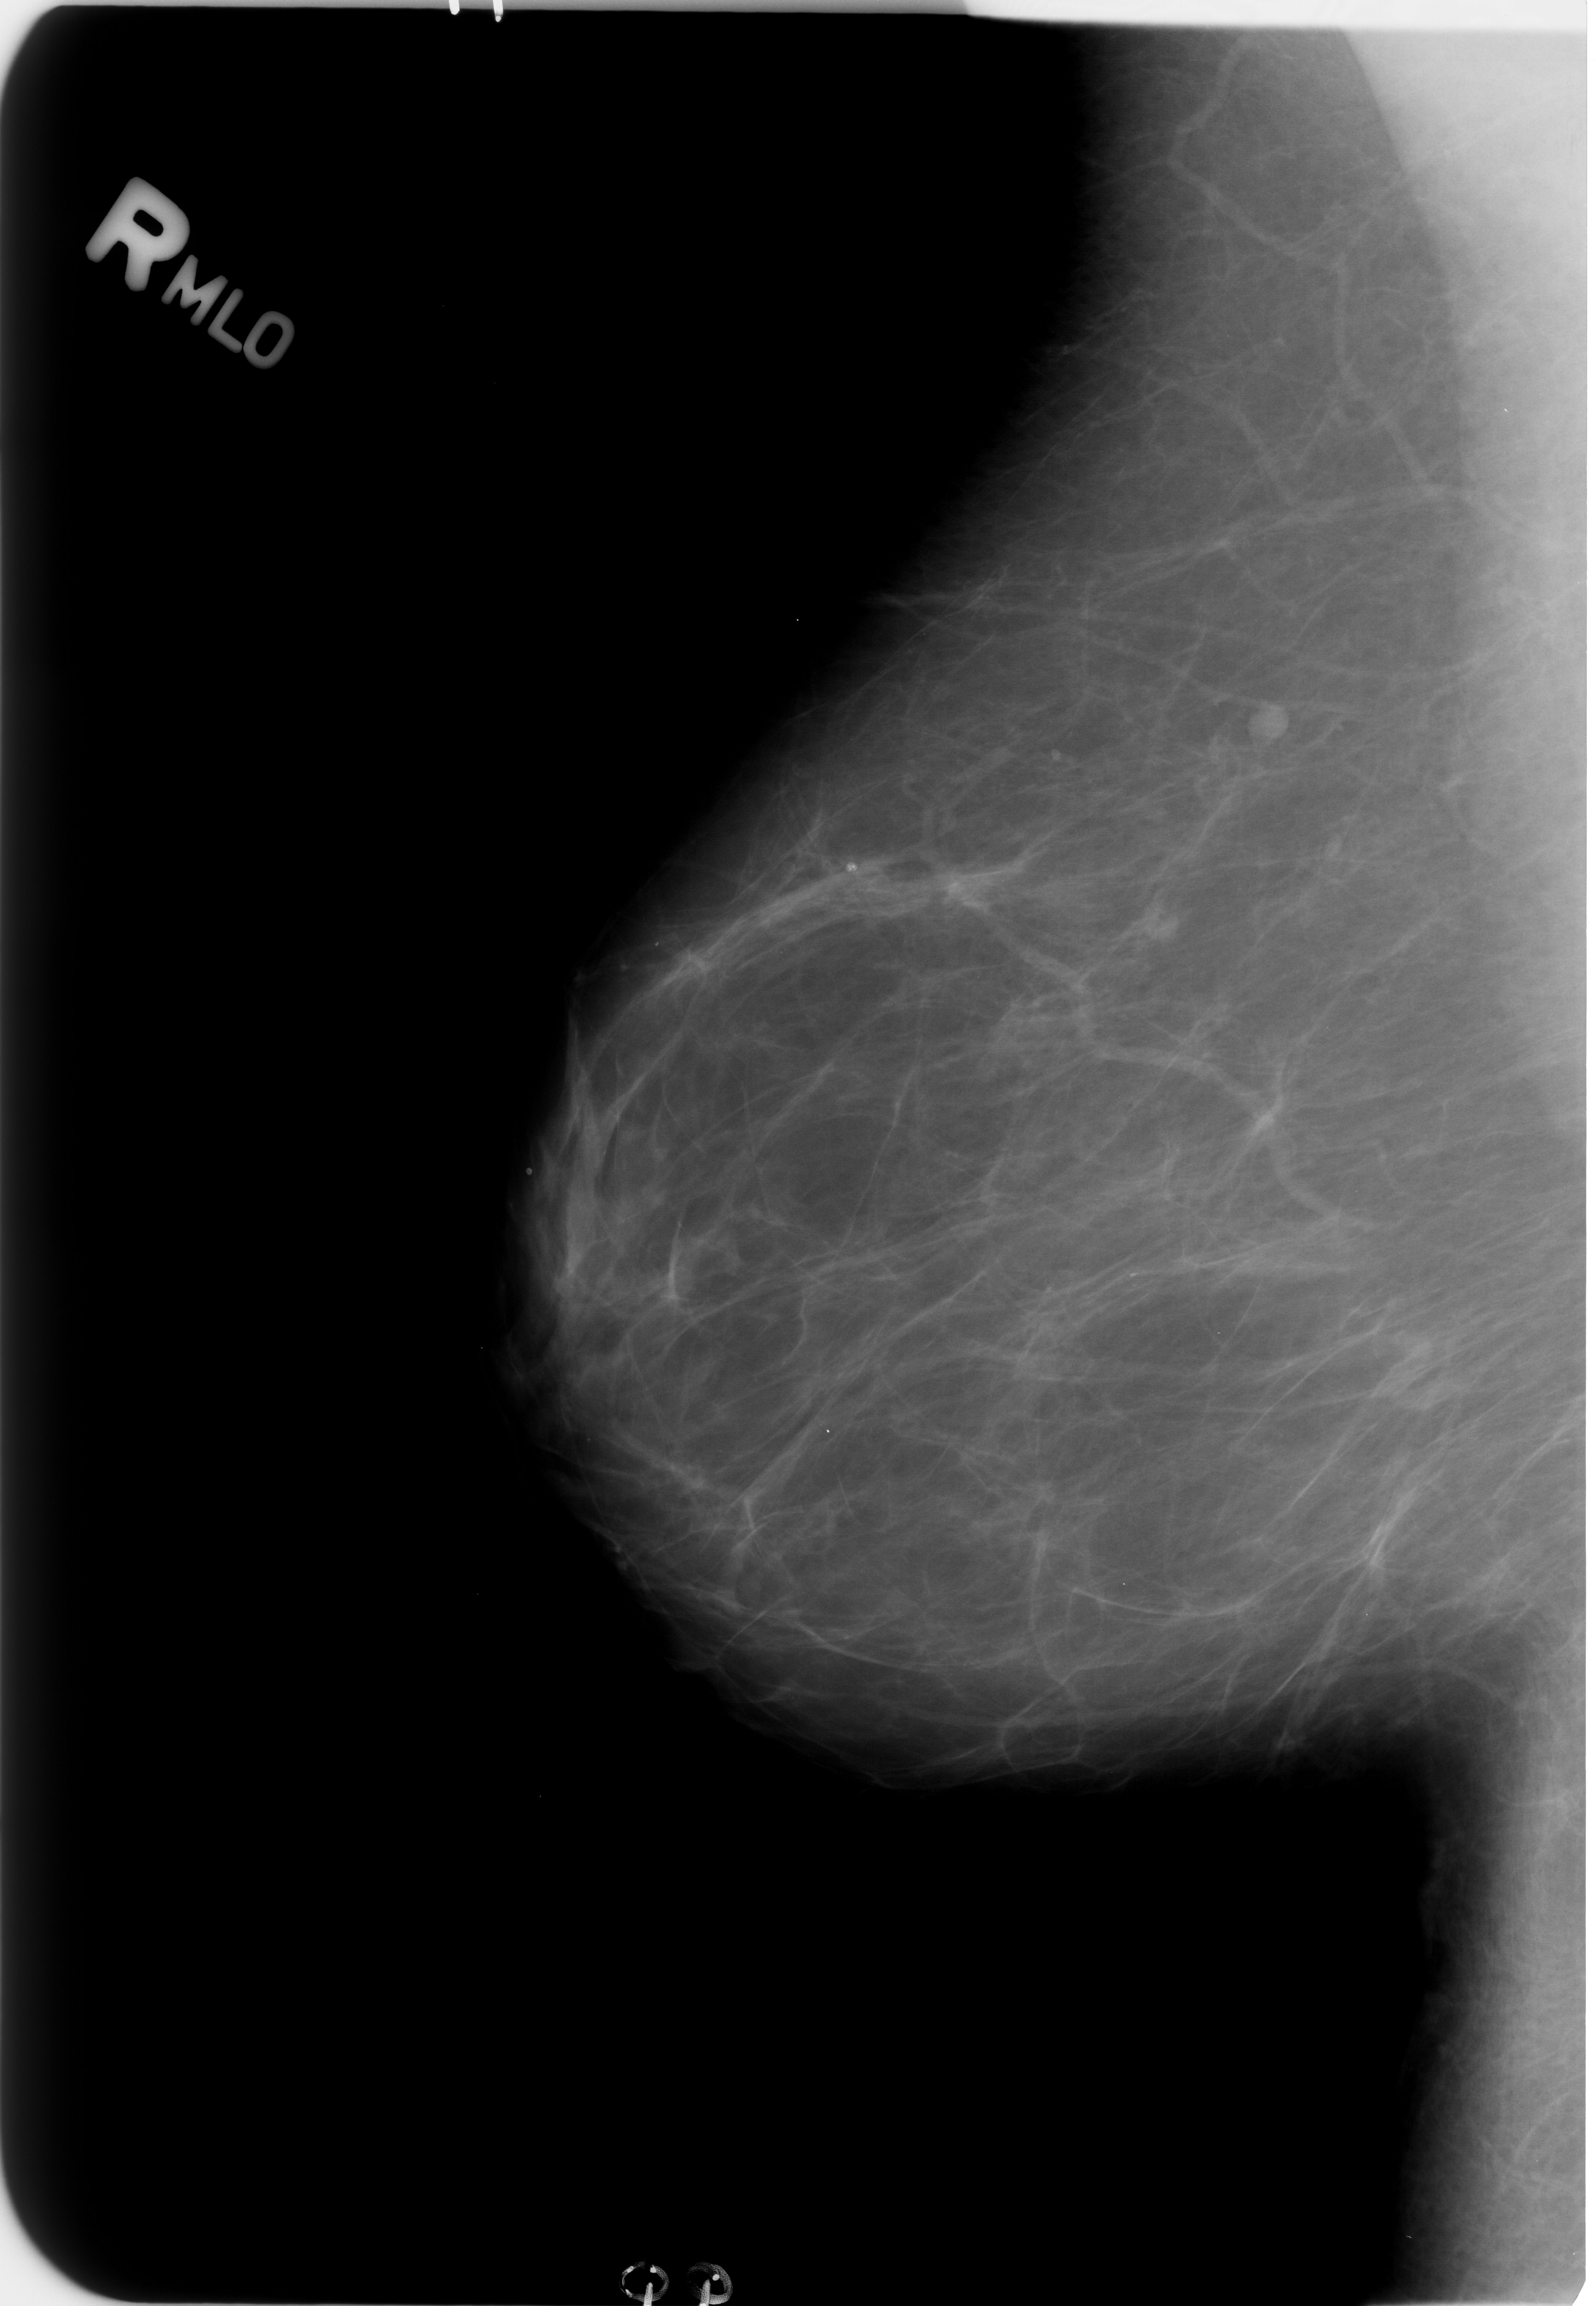
Mammogram (digitized film). Right breast. MLO view. 1596 × 2306 image matrix.
Expert-marked regions of interest on this film, with their recorded descriptors:
- Finding 1 of 3: mass, shape lymph node, margins circumscribed; BI-RADS assessment category 2; subtlety rating 4 on a 1 (subtle) to 5 (obvious) scale; outcome (as recorded, no biopsy): benign without callback (not worked up further): box from (x=820, y=847) to (x=882, y=891) px
- Finding 2 of 3: mass, shape lymph node, margins circumscribed; BI-RADS assessment category 2; benign; no additional work-up was recommended (outcome (as recorded, no biopsy): benign without callback): (x=1116, y=883)–(x=1193, y=953)
- Finding 3 of 3: mass, shape lymph node, margins circumscribed; BI-RADS assessment category 2; outcome (as recorded, no biopsy): benign without callback (not worked up further): (x=1253, y=703)–(x=1287, y=739)